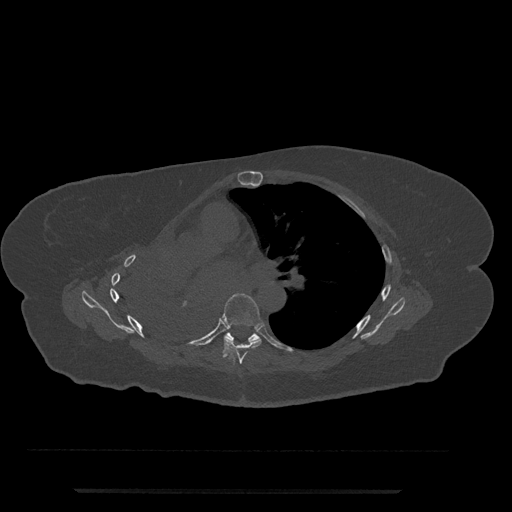
CT including the spine, one axial slice; slice 477 of 797 in the series (ordered by position); reconstruction kernel Br40s/3; 120 kVp; bone window (W 1800 / L 400 HU); 0.5 mm slice thickness; 512 × 512 image matrix, field of view 440 × 440 mm. Female patient, age 51 years. From the clinical record (not read from this slice): primary cancer: neuro.
Structures marked on this image (semi-automatically segmented with operator editing):
- T6 vertebra: bounding box <204,293,262,364> (left, top, right, bottom; pixels)
- T7 vertebra: <225,333,261,341>